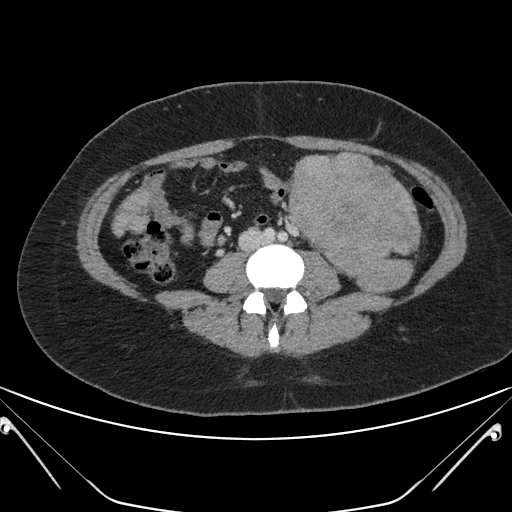
Contrast-enhanced abdominal CT, one axial slice. 120 kVp. Intravenous contrast given. Soft-tissue window (W 400 / L 40 HU). 512 × 512 image matrix. Female patient, age 26 years. Case-level facts recorded for this patient, not image findings: diagnosis: adrenocortical carcinoma; tumour side: left adrenal; tumour size at pathology: 28 cm; Ki-67 index: 20 %; stage (as recorded): 2.
Outlined on this slice (semi-automatically segmented with operator editing):
- mass: bounding box [x1, y1, x2, y2] px = [288, 152, 420, 292]